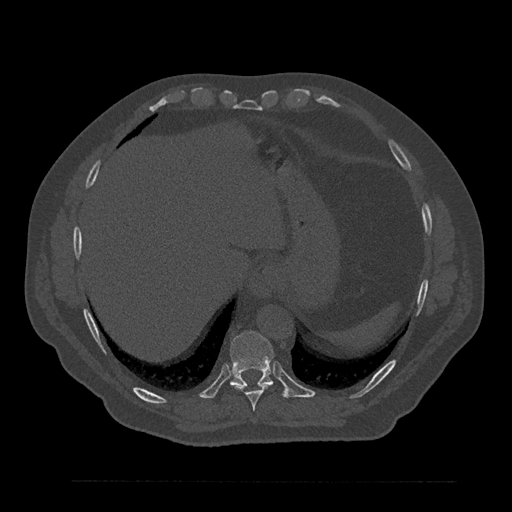
CT including the spine, one axial slice. Position 378 of 797 along the scan axis. Reconstruction kernel Br40s/3. Bone window (W 1800 / L 400 HU). 0.5 mm slice thickness. 512 × 512 image matrix, field of view 430 × 430 mm. Patient: male, 61 years. From the clinical record (not read from this slice): primary cancer: prostate.
Annotated regions visible in this slice (semi-automatically segmented with operator editing):
- T10 vertebra: bounding box <230,331,274,386> (left, top, right, bottom; pixels)
- T9 vertebra: <232,383,273,411>